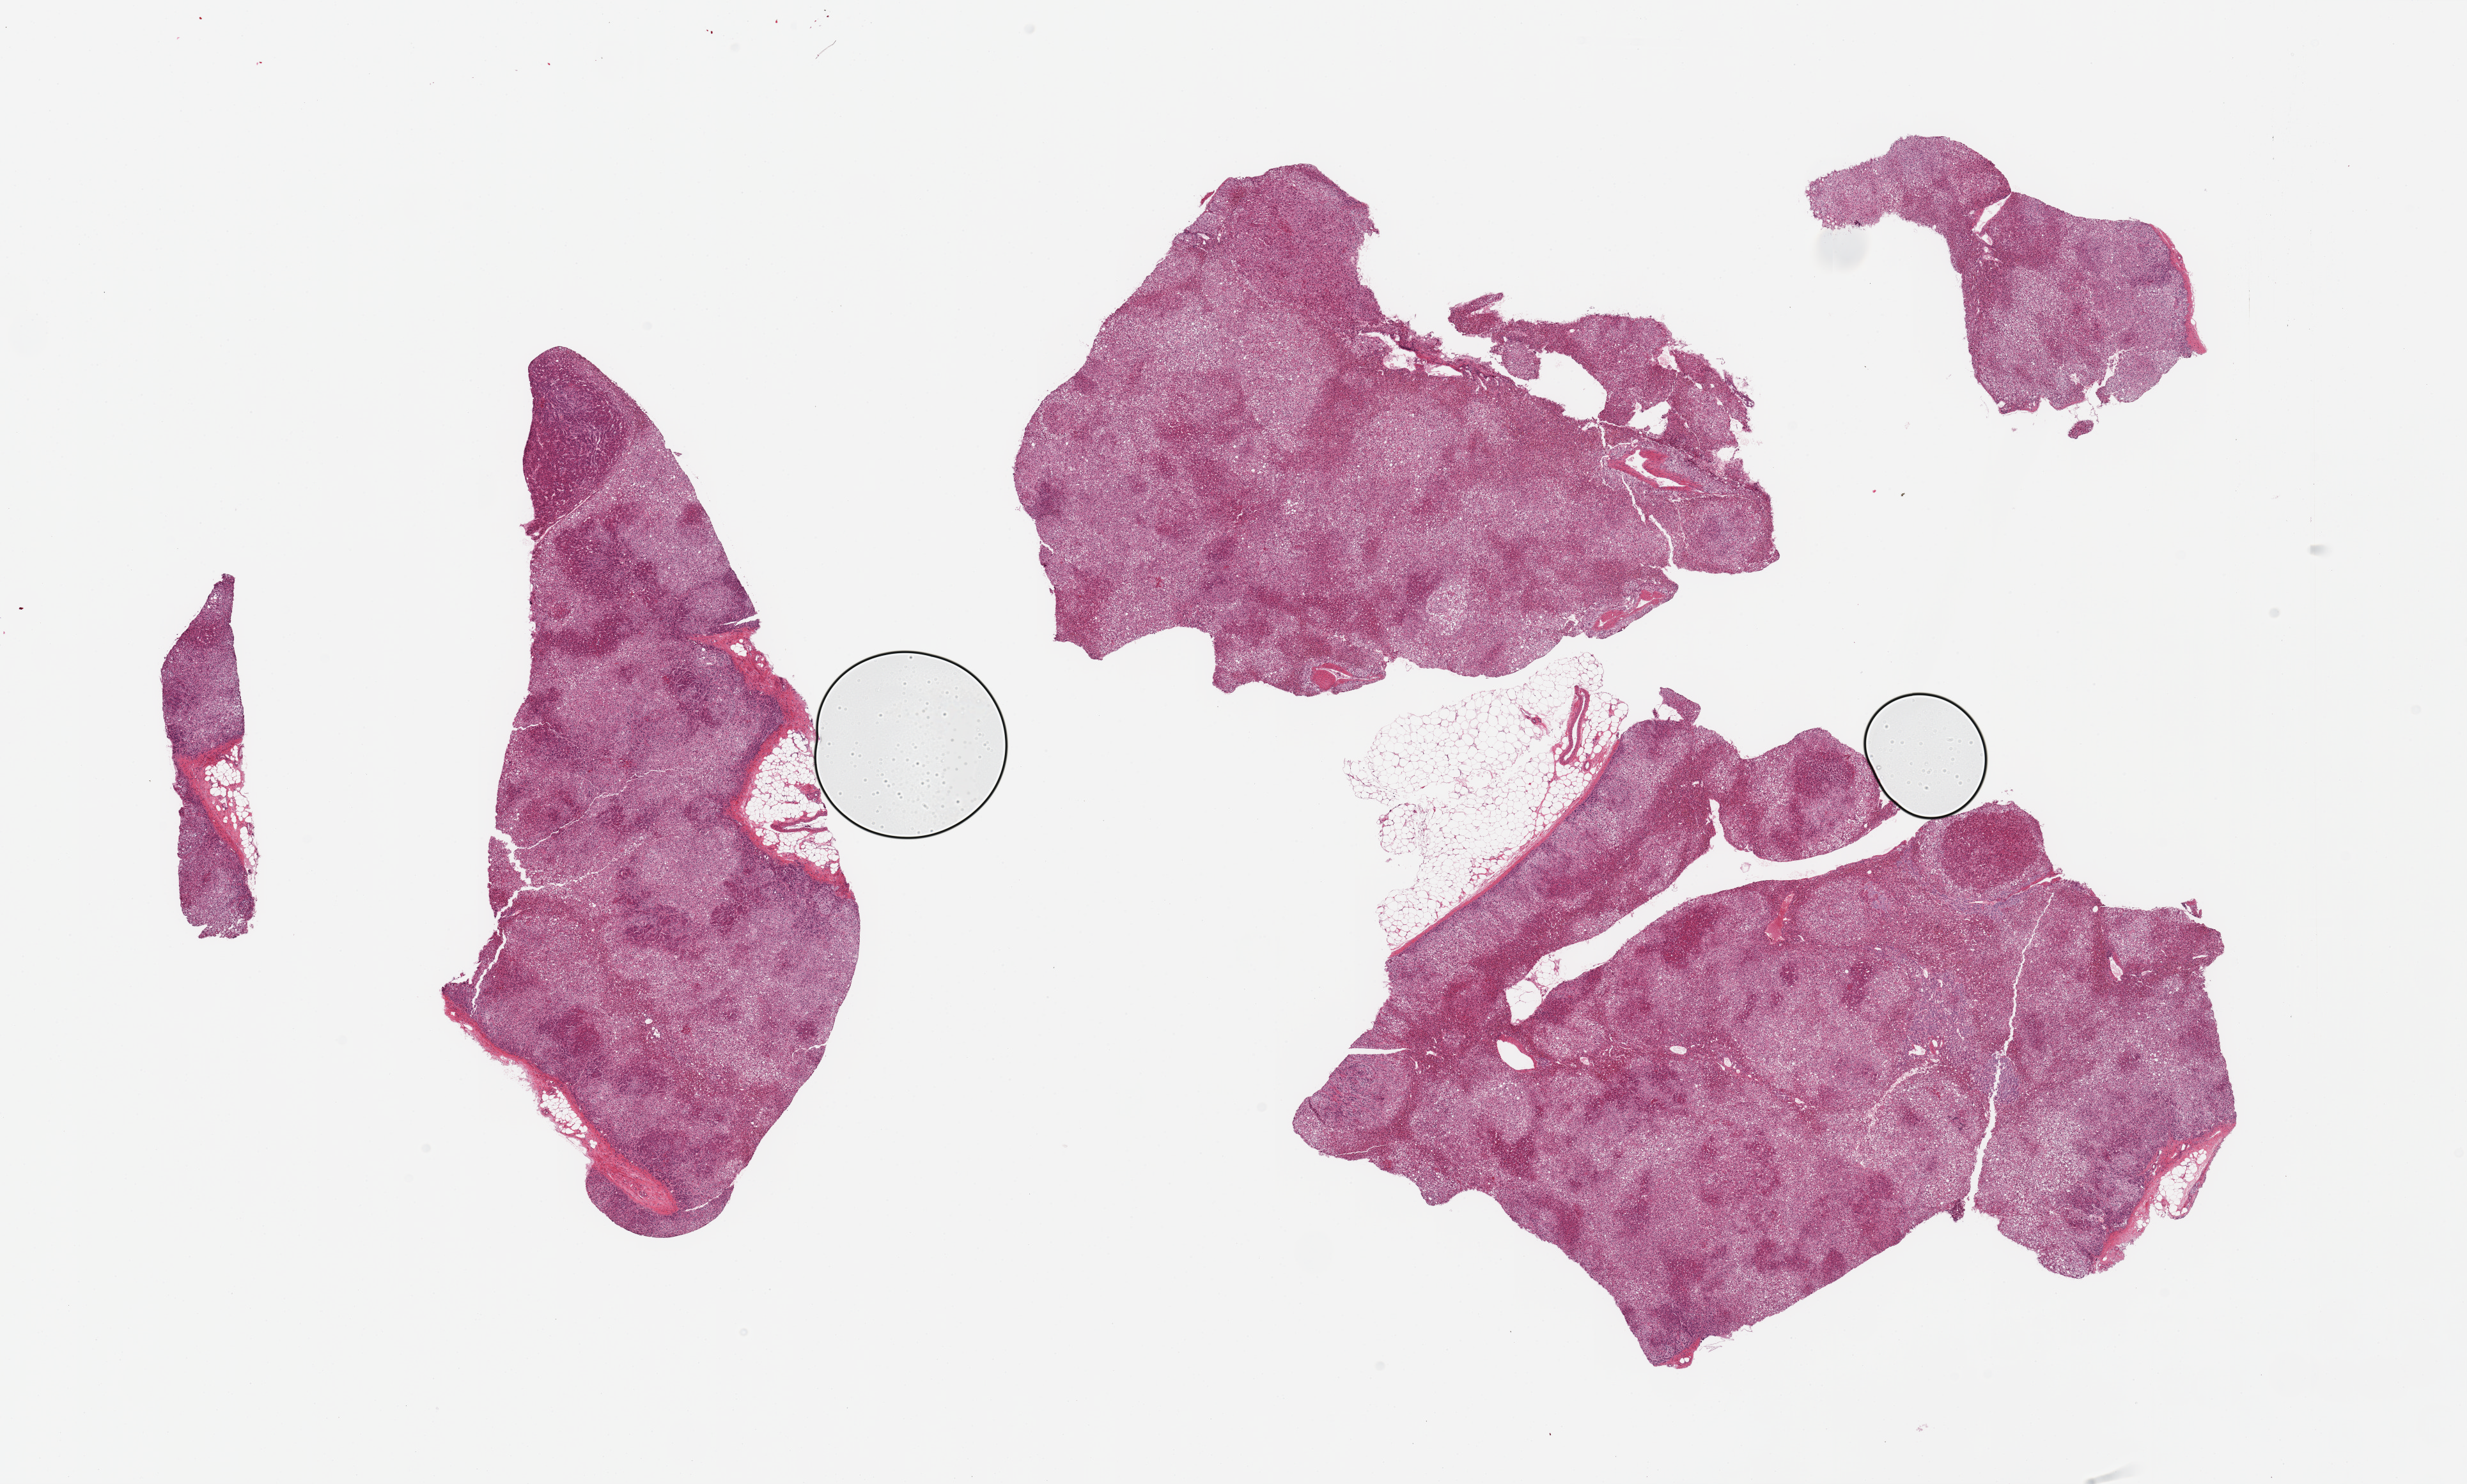
Digitized hematoxylin and eosin (H&E)-stained section, brightfield, low-resolution overview of the scanned area, about 30.5 x 18.4 mm, PAXgene-fixed paraffin-embedded (PFPE) section, sampled site (target tissue): adrenal gland, tissue donor sample. Donor sex: male.
Pathologist's review note for this sample: 3 pieces plus fragments; 10% external fat.